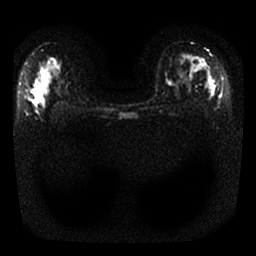
Breast MRI, one axial slice. Diffusion-weighted series; image 2 of 4 stored at this slice position (different b-values; order by instance number). 1.5 T. 4 mm slice thickness. 256 × 256 image matrix, field of view 320 × 320 mm. Female patient.
Annotated regions visible in this slice (outlined manually by an expert reader):
- tumour on diffusion-weighted imaging: box from (x=197, y=61) to (x=211, y=88) px